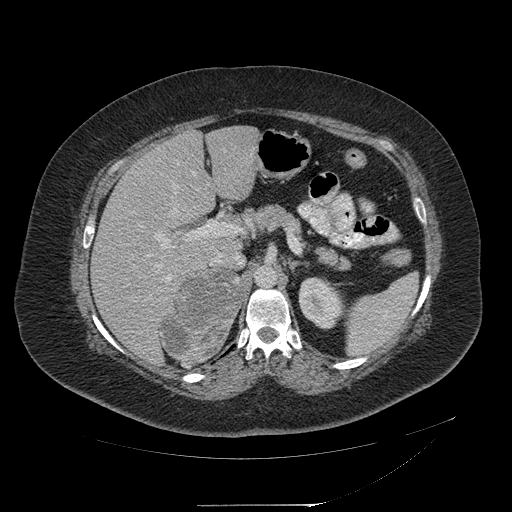
Contrast-enhanced abdominal CT, one axial slice; slice 134 of 217 in the series (ordered by position); 120 kVp; intravenous contrast given; soft-tissue window (W 400 / L 40 HU); 1.25 mm slice thickness; 512 × 512 image matrix, field of view 453 × 453 mm. Female patient, age 55 years. Case-level facts recorded for this patient, not image findings: diagnosis: adrenocortical carcinoma; tumour side: right adrenal; tumour size at pathology: 11 cm; Ki-67 index: 20 %.
Outlined on this slice (semi-automatically segmented with operator editing):
- mass: box from (x=161, y=270) to (x=240, y=363) px